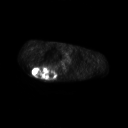
FDG PET of an extremity soft-tissue mass (from a PET/CT study), one axial slice; position 191 of 267 along the scan axis; 3.27 mm slice thickness; 128 × 128 image matrix, field of view 700 × 700 mm. Male patient, age 61 years. From the clinical record (not read from this slice): histological type: pleiomorphic spindle cell undifferentiated; grade: high; site of the primary tumour: right parascapusular.
Structures marked on this image (expert contour drawn on MRI and transferred to this co-registered scan by the dataset authors):
- gross tumour volume including surrounding oedema: bounding box (x1, y1, x2, y2) in pixels: (32, 65, 59, 79)
- gross tumour volume (mass): (32, 65, 56, 78)